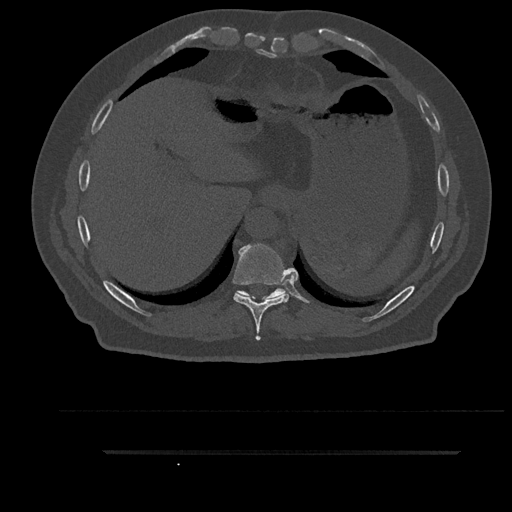
CT including the spine, one axial slice; slice 408 of 797 in the series (ordered by position); reconstruction kernel Br40s/3; 120 kVp; bone window (W 1800 / L 400 HU); 512 × 512 image matrix. Male patient, age 63 years. Case-level facts recorded for this patient, not image findings: primary cancer: renal.
Structures marked on this image (semi-automatic segmentation, software-assisted and operator-edited):
- T10 vertebra: bounding box [x1, y1, x2, y2] px = [235, 288, 286, 300]
- T9 vertebra: [233, 244, 290, 341]